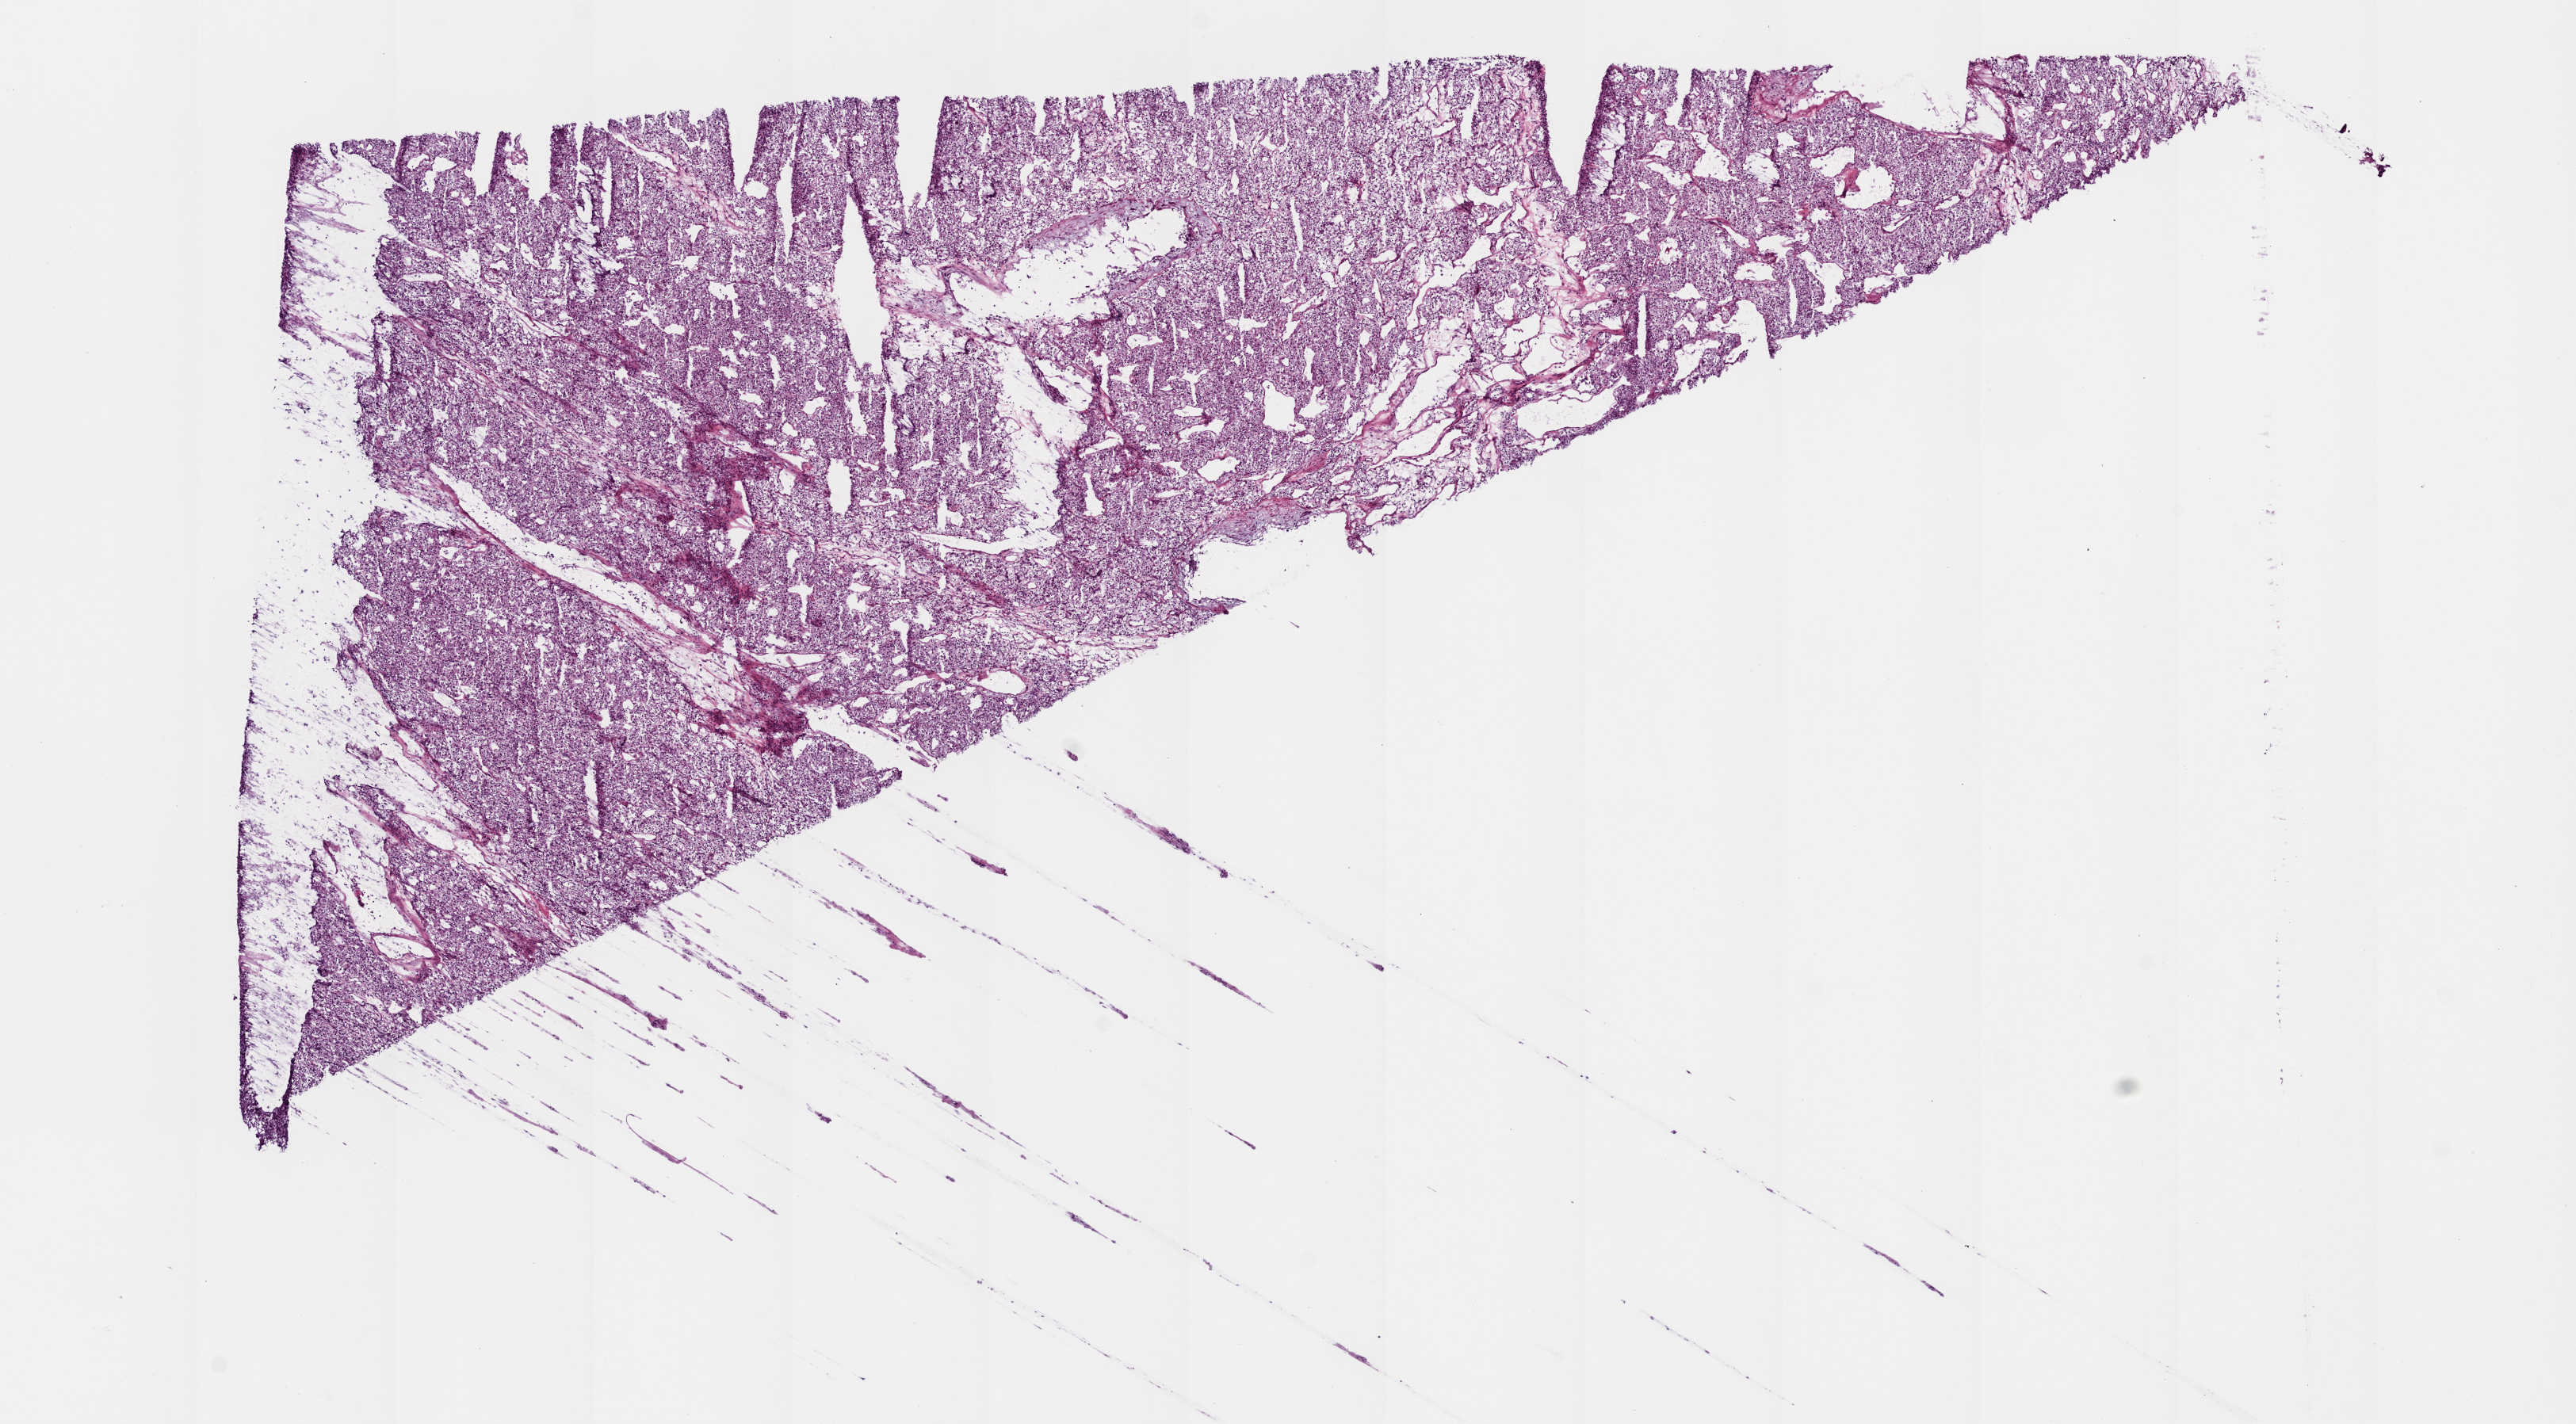
Digitized Hematoxylin and eosin (H&E) stained tissue section (whole slide) — whole scanned area (about 13.0 x 7.2 mm) shown as a low-resolution overview, frozen section from the top of the tissue portion, primary tumour sample from the kidney. Male patient; age at initial diagnosis 74 years. Histologic grade: G3 (poorly differentiated). Slide review estimates, as recorded: tumour cells 95%, tumour nuclei 90%, normal cells 0%, stromal cells 5%, necrosis 0%.
• laterality: right
• AJCC pathologic stage: III
• diagnosis: Clear cell adenocarcinoma, NOS
• lymph nodes positive (case pathology): 2 of 2 examined